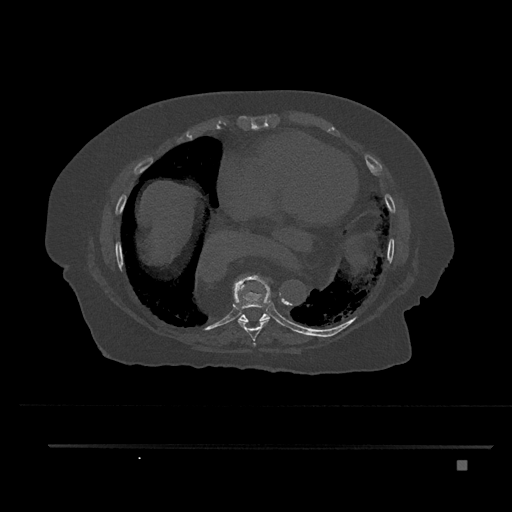
CT including the spine, one axial slice. Reconstruction kernel Br40s/3. 120 kVp. Bone window (W 1800 / L 400 HU). 0.5 mm slice thickness. 512 × 512 image matrix. Female patient, age 76 years. From the clinical record (not read from this slice): primary cancer: lung; vertebrae with lytic lesions (as recorded): T11, L3.
Annotated regions visible in this slice (semi-automatically segmented with operator editing):
- T7 vertebra: bounding box (x1, y1, x2, y2) in pixels: (253, 343, 255, 345)
- T8 vertebra: (232, 274, 271, 346)
- T9 vertebra: (237, 275, 271, 322)